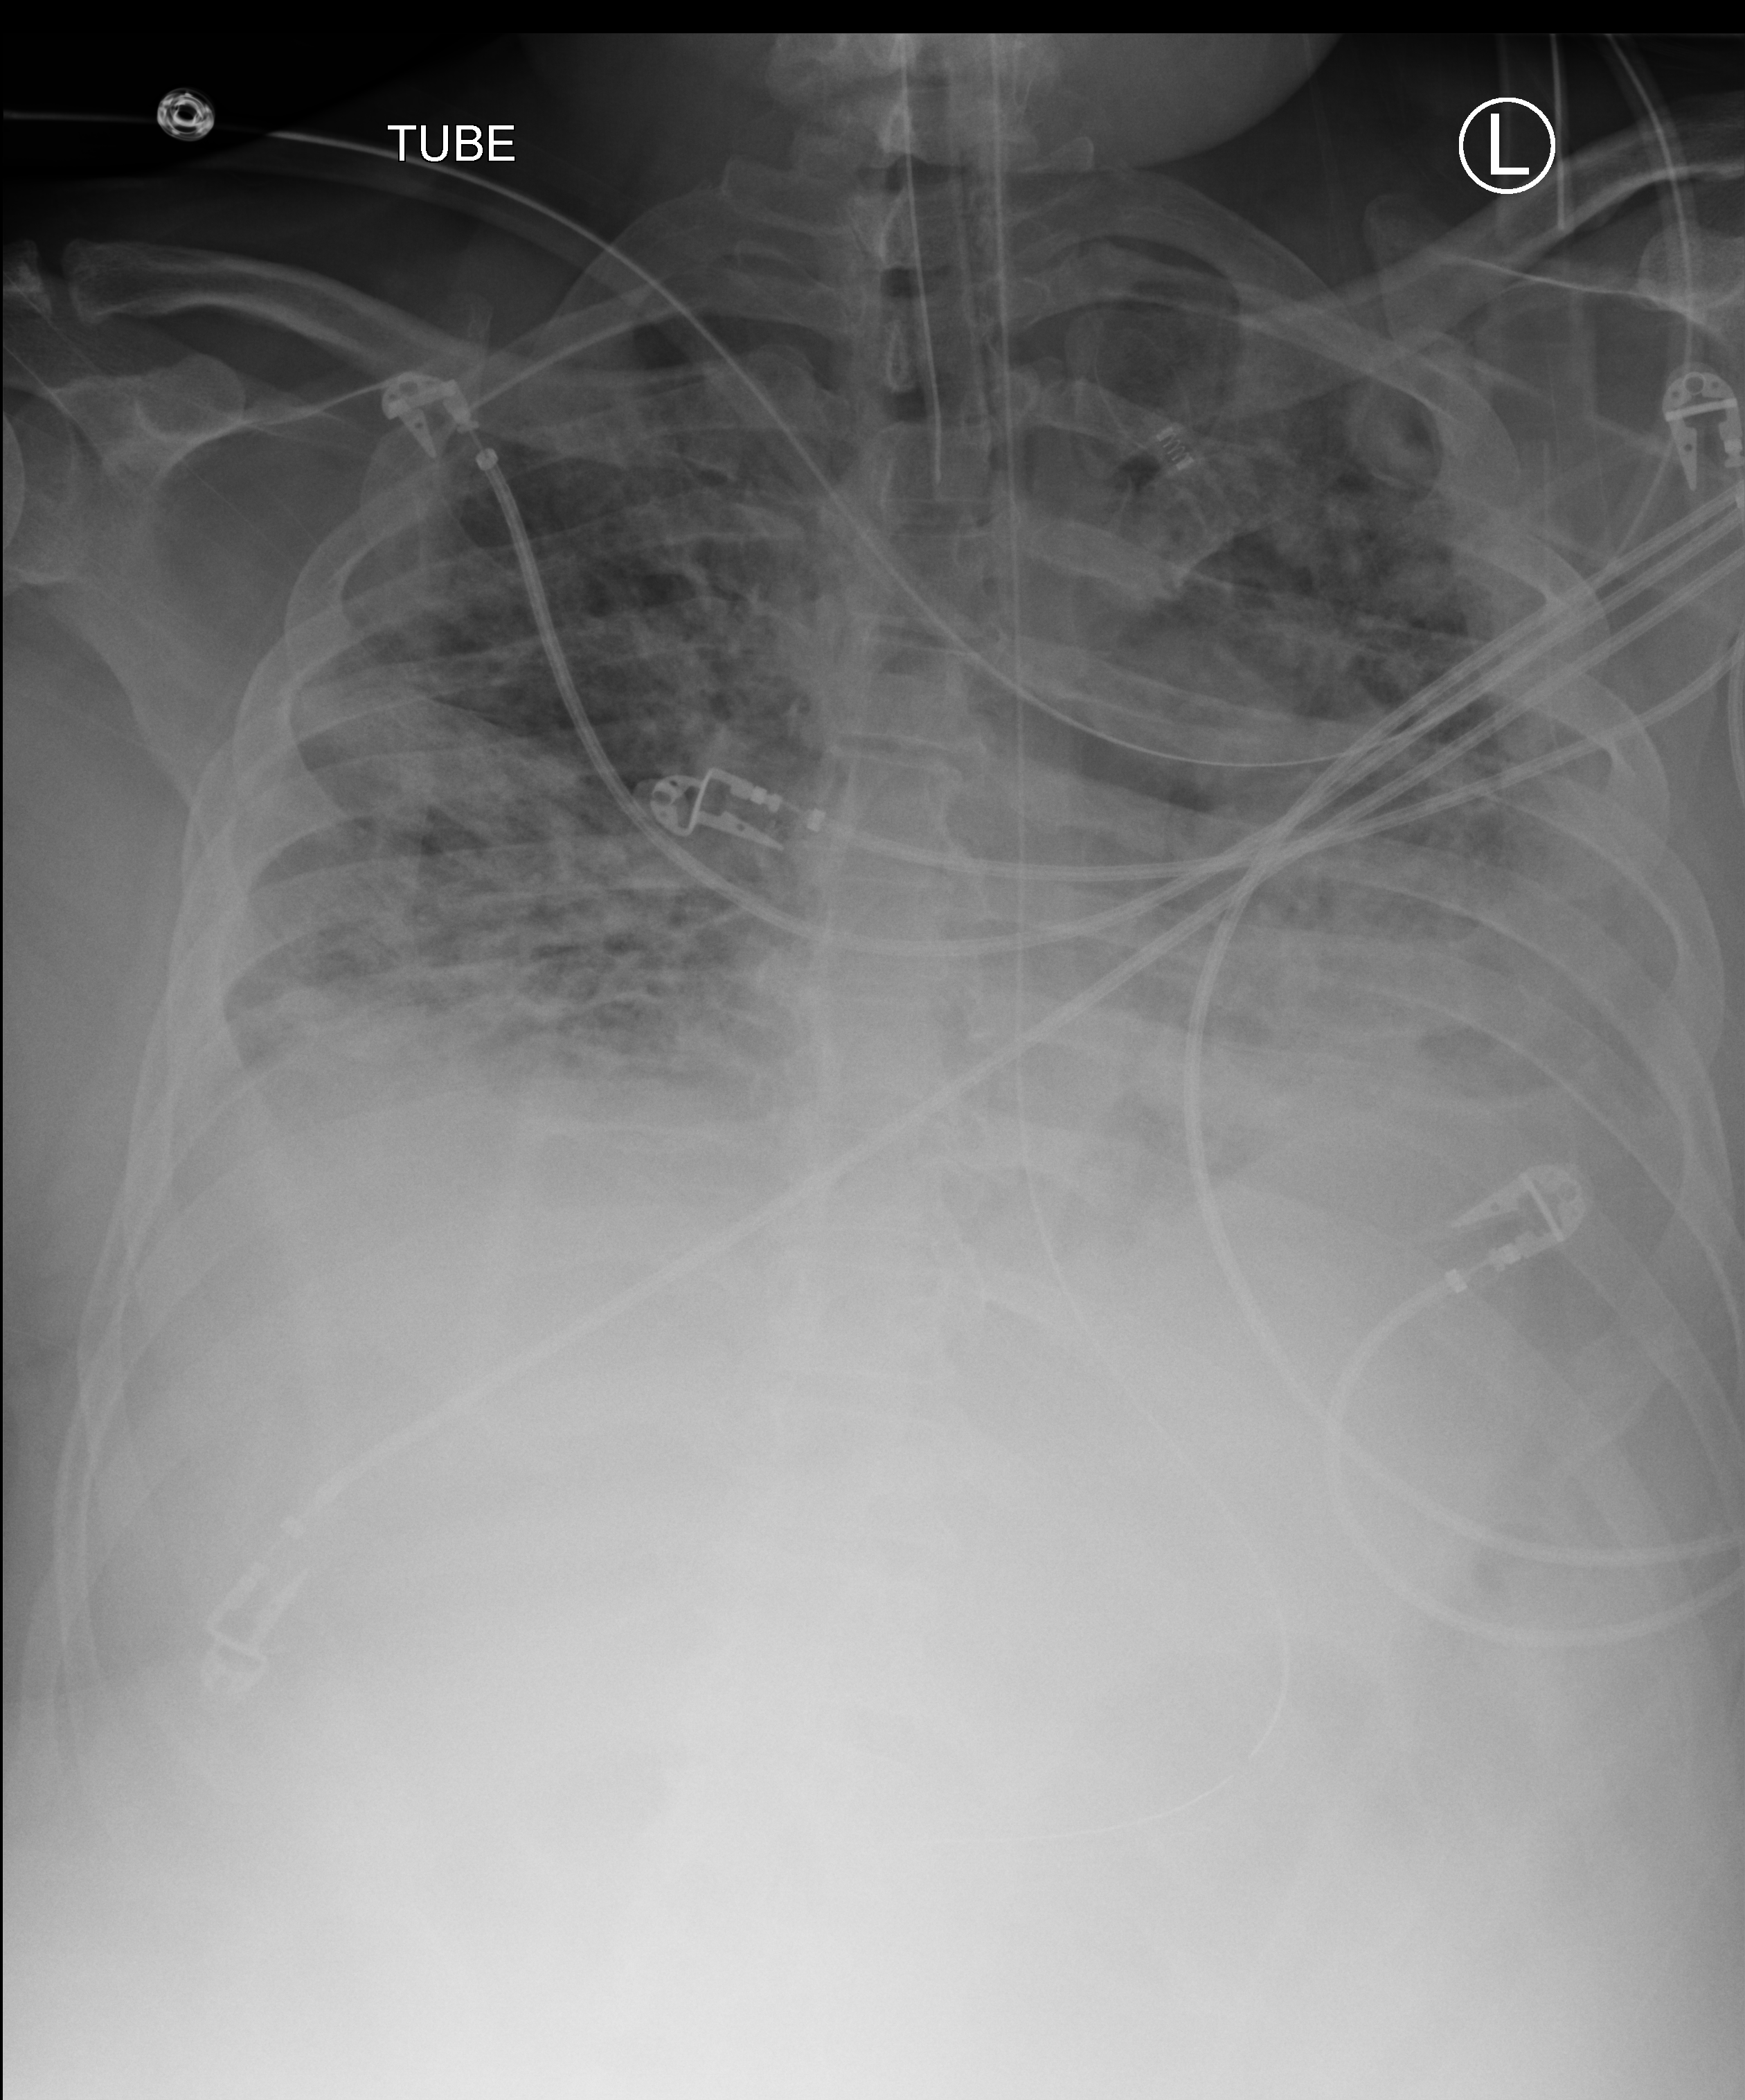
Chest X-ray (portable); anteroposterior (AP) projection. Male patient hospitalised with COVID-19, age 18–59 years.
From the hospital-stay record, not from the radiograph (when in the stay this image was taken is not recorded):
- mechanically ventilated during this hospital stay: yes
- length of hospital stay: 22 days
- admitted to intensive care during this hospital stay: yes